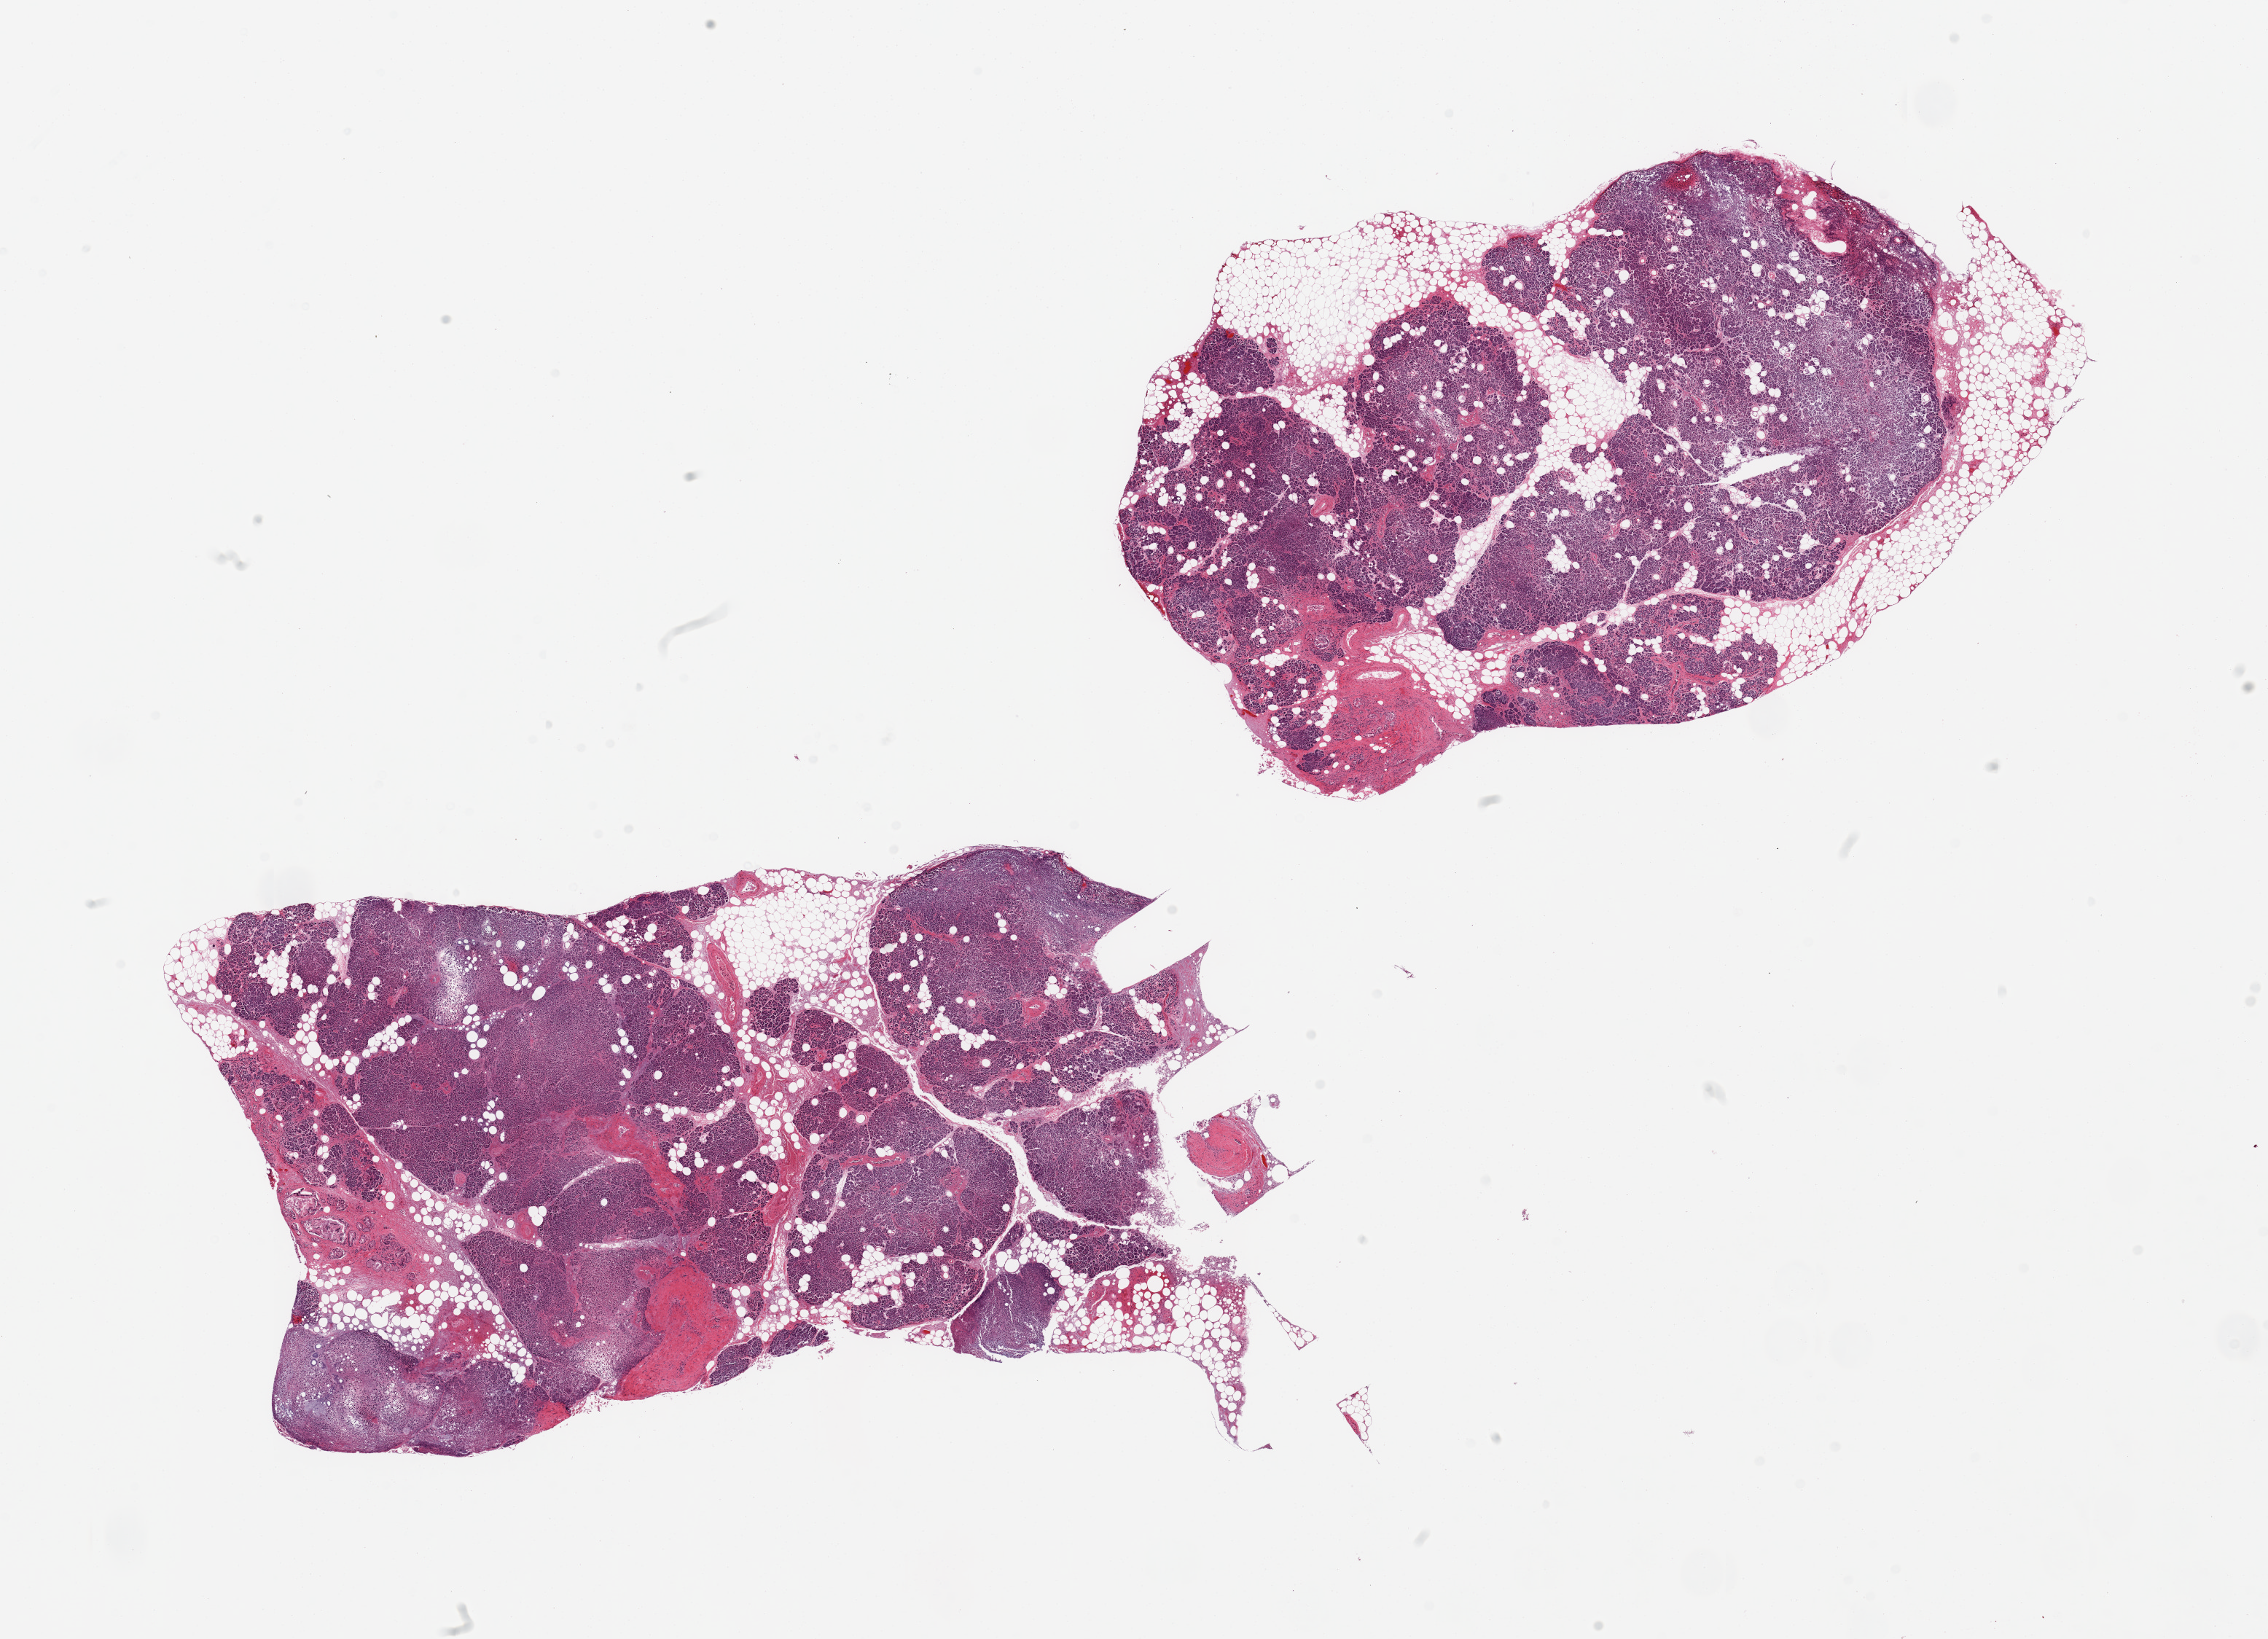
Digitized H&E-stained section, whole scanned area (about 24.6 x 17.8 mm) shown as a low-resolution overview, PAXgene-fixed, paraffin-embedded tissue, sampled site (target tissue): pancreas, tissue donor sample. Donor sex: male.
Reviewer comment on this tissue sample: 2 pieces; 20% internal and external fat.